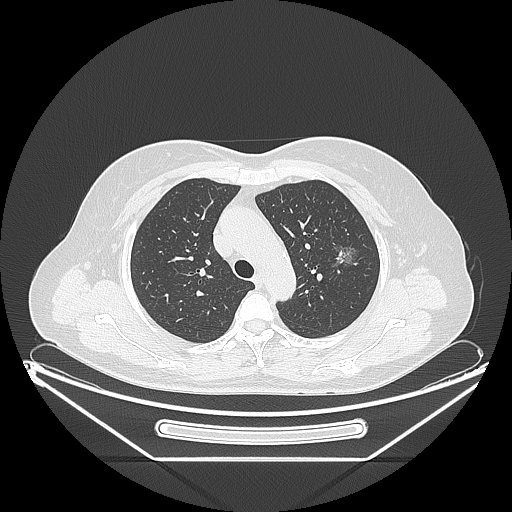
Chest CT, one axial slice; position 158 of 226 along the scan axis; 120 kVp; lung window (W 1500 / L -600 HU); 1.25 mm slice thickness; 512 × 512 image matrix. Female patient, age 54 years. Case-level facts recorded for this patient, not image findings: clinical TNM (as recorded): T1c N0 M0; histopathological grade: G1.
Annotated regions visible in this slice (bounding box drawn by a radiologist):
- lung tumour (recorded histology: adenocarcinoma): bounding box (x1, y1, x2, y2) in pixels: (321, 236, 363, 276)